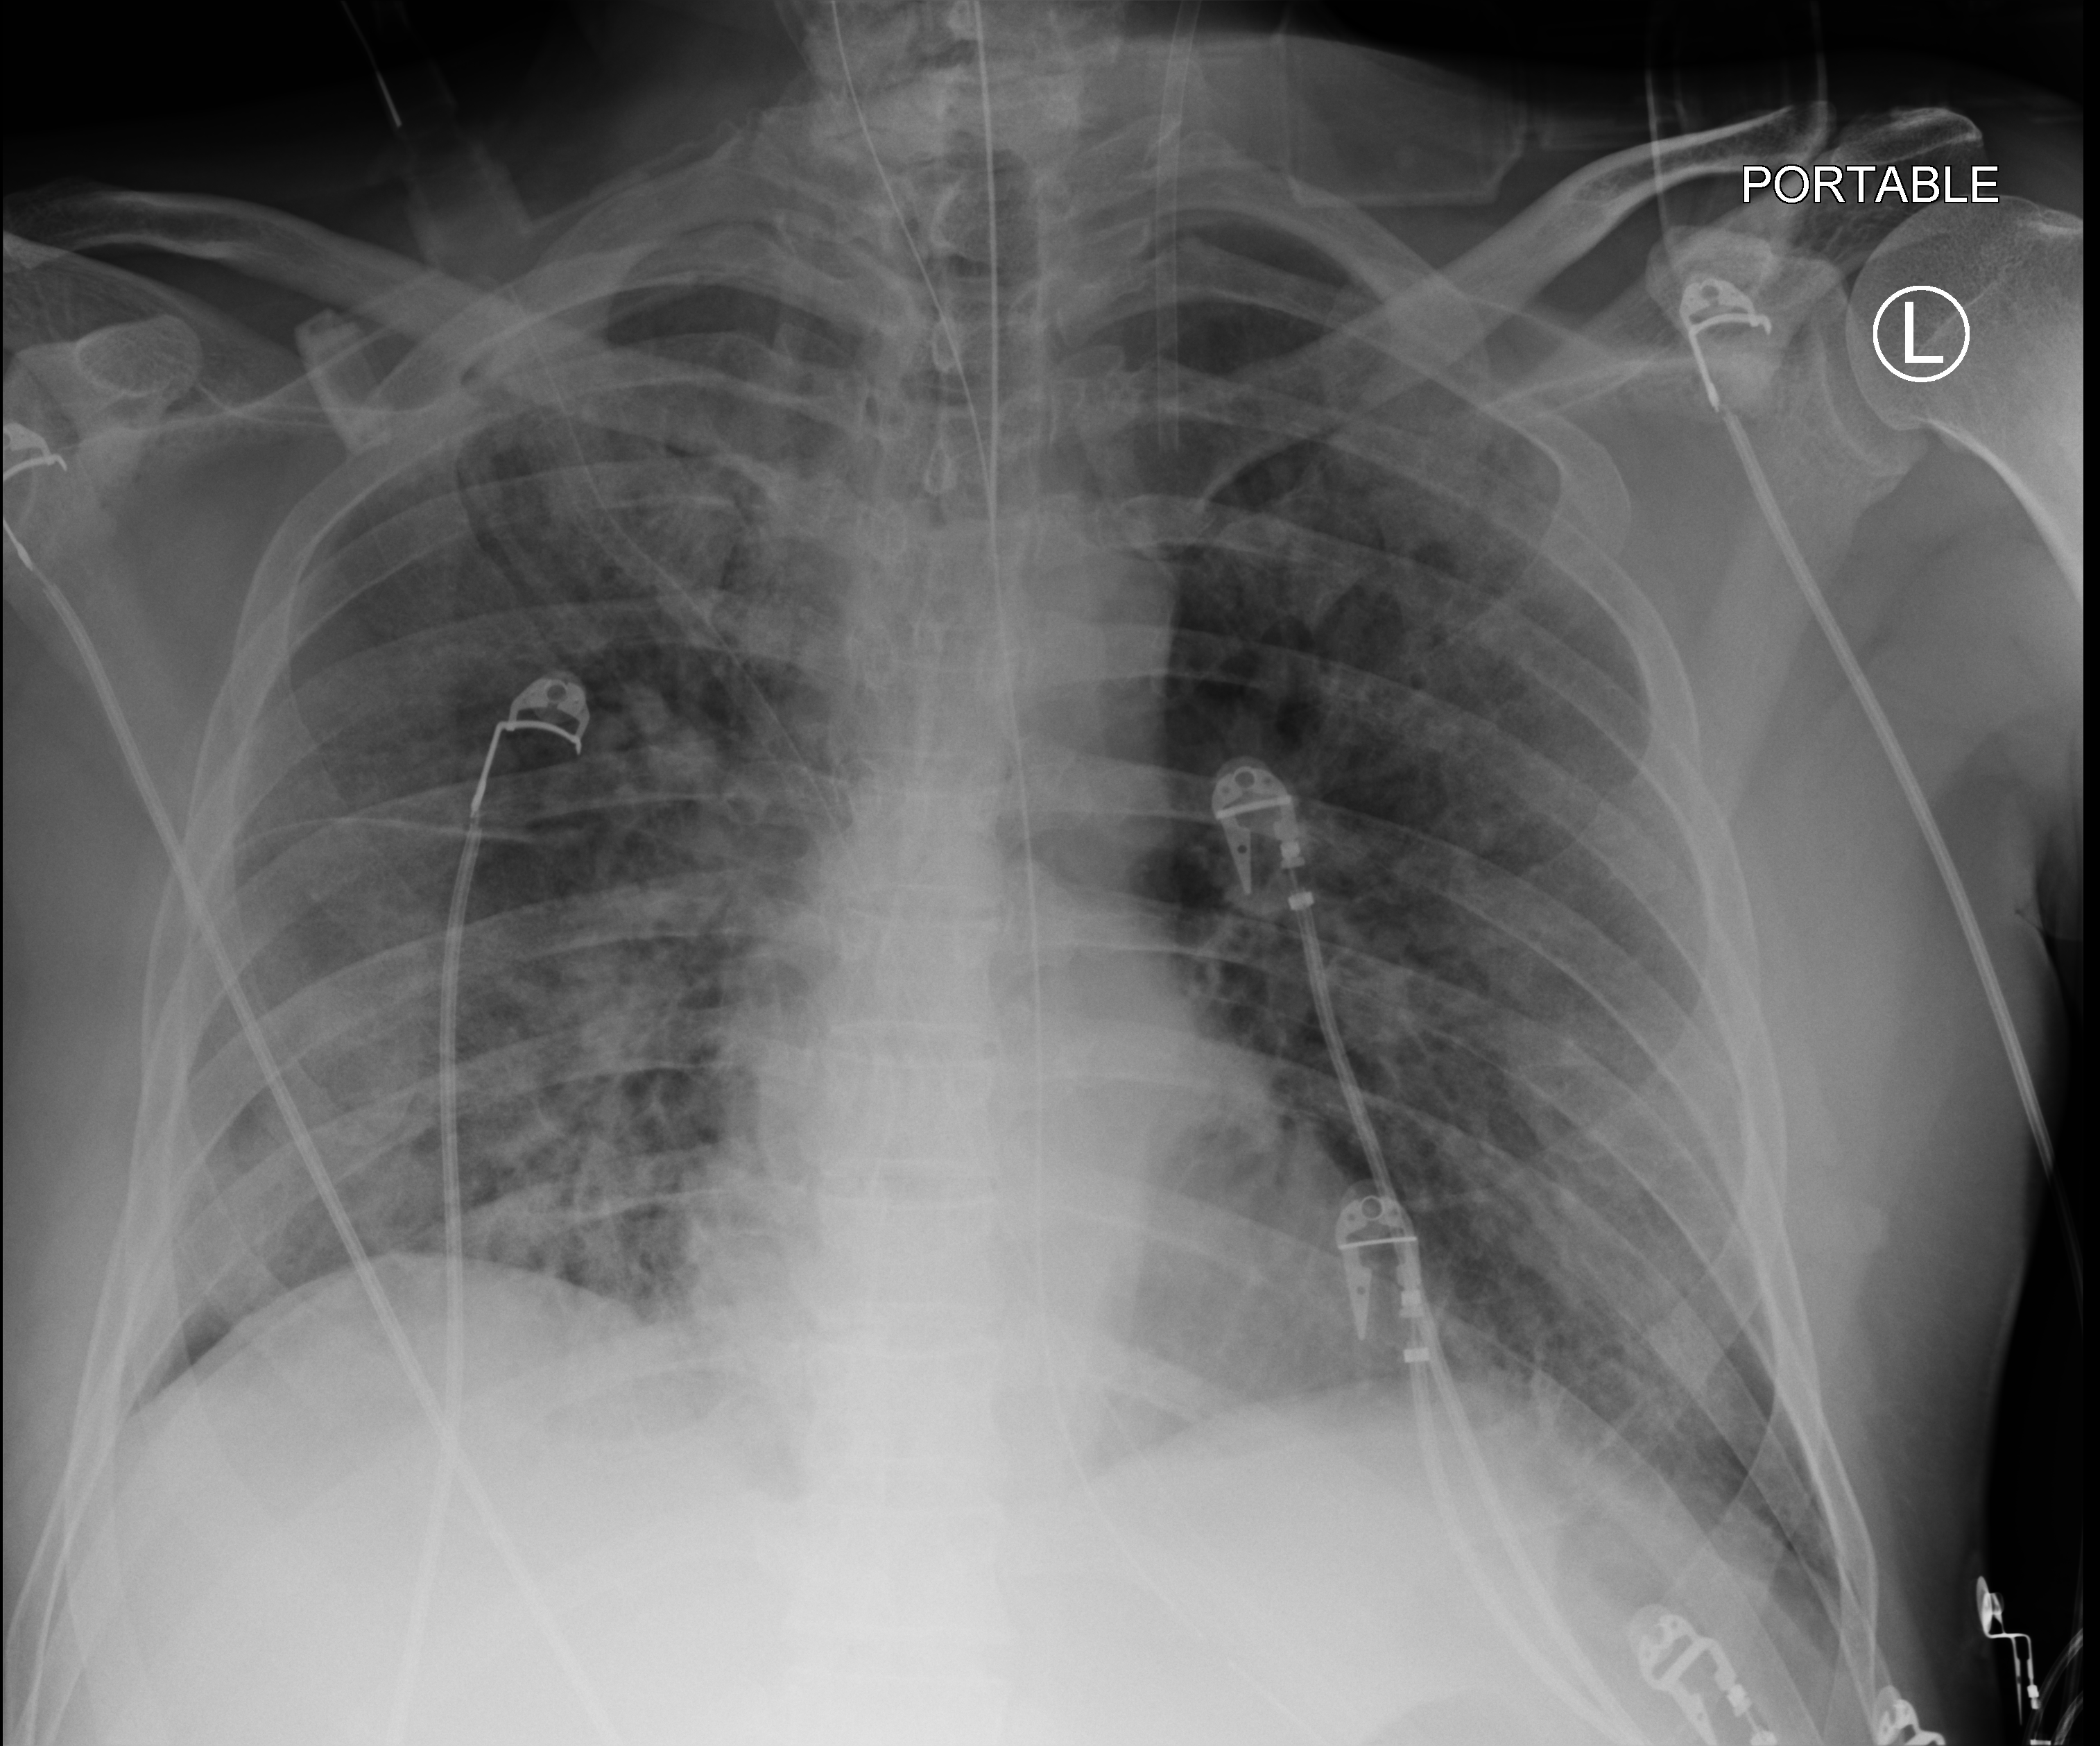
Chest X-ray (portable), anteroposterior (AP) projection. Male patient hospitalised with COVID-19, age 60–74 years.
Admission-level facts for this patient (not findings on this image; timing relative to this image not recorded): length of hospital stay: 8 days.